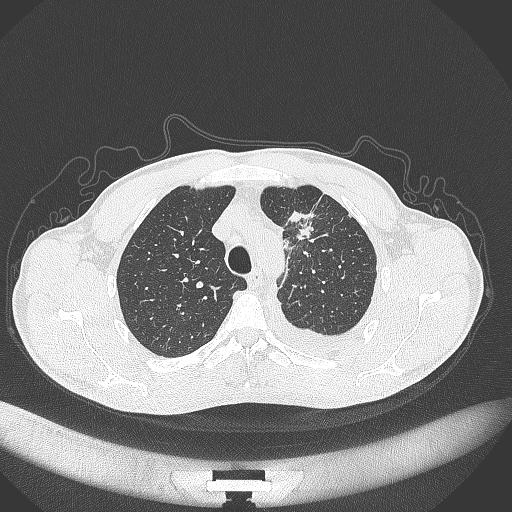
Chest CT, one axial slice. Slice 268 of 371 in the series (ordered by position). Reconstruction kernel B70f. 120 kVp. Lung window (W 1500 / L -600 HU). 1 mm slice thickness. 512 × 512 image matrix, field of view 400 × 400 mm. Patient: male, 49 years. Case-level facts recorded for this patient, not image findings: clinical TNM (as recorded): T1c N1 M1.
Outlined on this slice (bounding box drawn by a radiologist):
- lung tumour (recorded histology: adenocarcinoma): bounding box <284,208,319,245> (left, top, right, bottom; pixels)